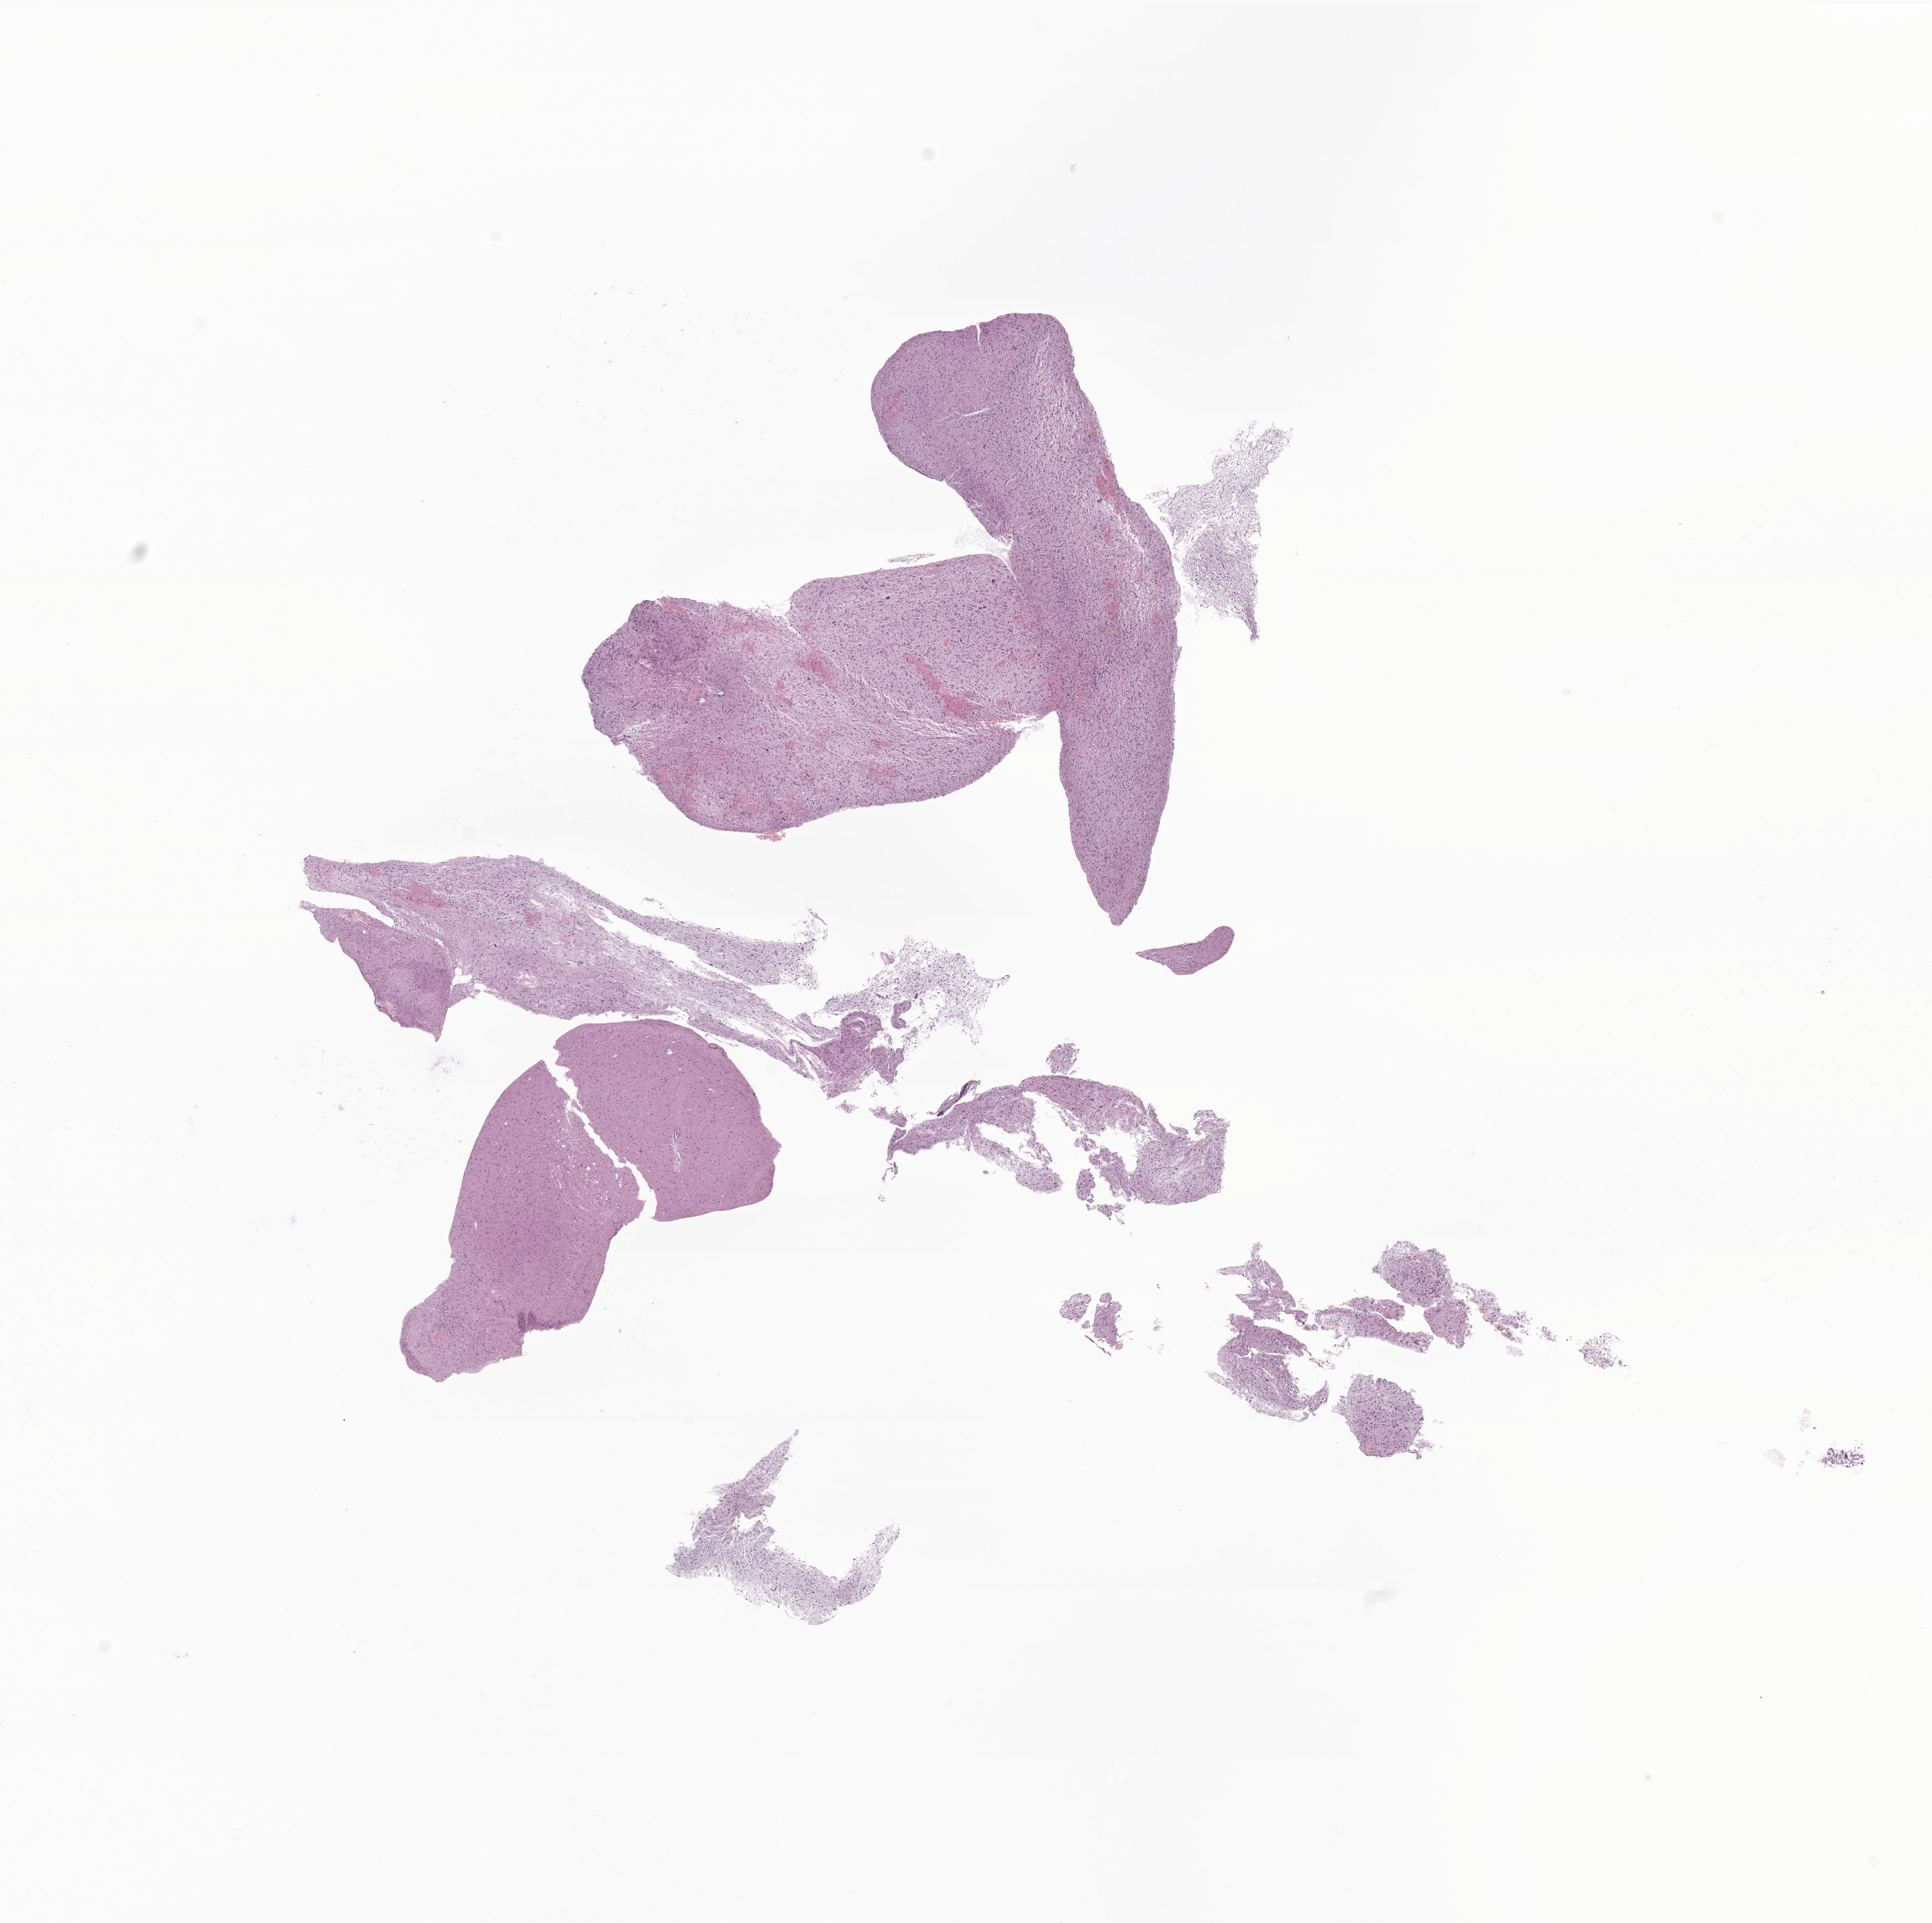
Digitized haematoxylin and eosin-stained section of tumor tissue from the brain, shown as a low-resolution overview of the whole scanned area (about 12.2 x 12.2 mm). Formalin-fixed, paraffin-embedded (FFPE) tissue. Patient male; age 74 months (6 years 2 months).
* diagnosis (ICD-O-3 morphology term): Glioma, malignant